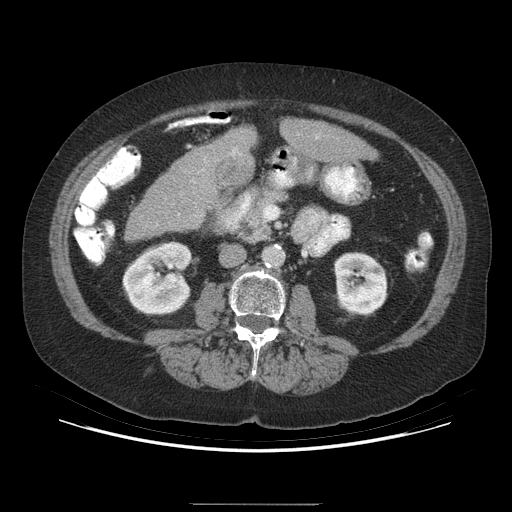
Contrast-enhanced abdominal CT (liver protocol), one axial slice. Slice 132 of 192 in the series (ordered by position). Soft-tissue window (W 400 / L 40 HU). 2.5 mm slice thickness. 512 × 512 image matrix, field of view 400 × 400 mm. From the clinical record (not read from this slice): diagnosis: hepatocellular carcinoma (patient treated with transarterial chemoembolisation; whether this scan precedes or follows treatment is not stated here); TNM stage (as recorded): Stage-I; Child-Pugh class: A; tumour differentiation: moderately differentiated; tumour nodularity: uninodular.
Annotated regions visible in this slice (semi-automatically segmented with operator editing):
- liver parenchyma outside the tumour (the mass and vessels are separate outlines, so this box may not span the whole liver): bounding box <127,120,376,238> (left, top, right, bottom; pixels)
- mass: <217,155,256,188>
- liver vessels: <233,151,235,153>